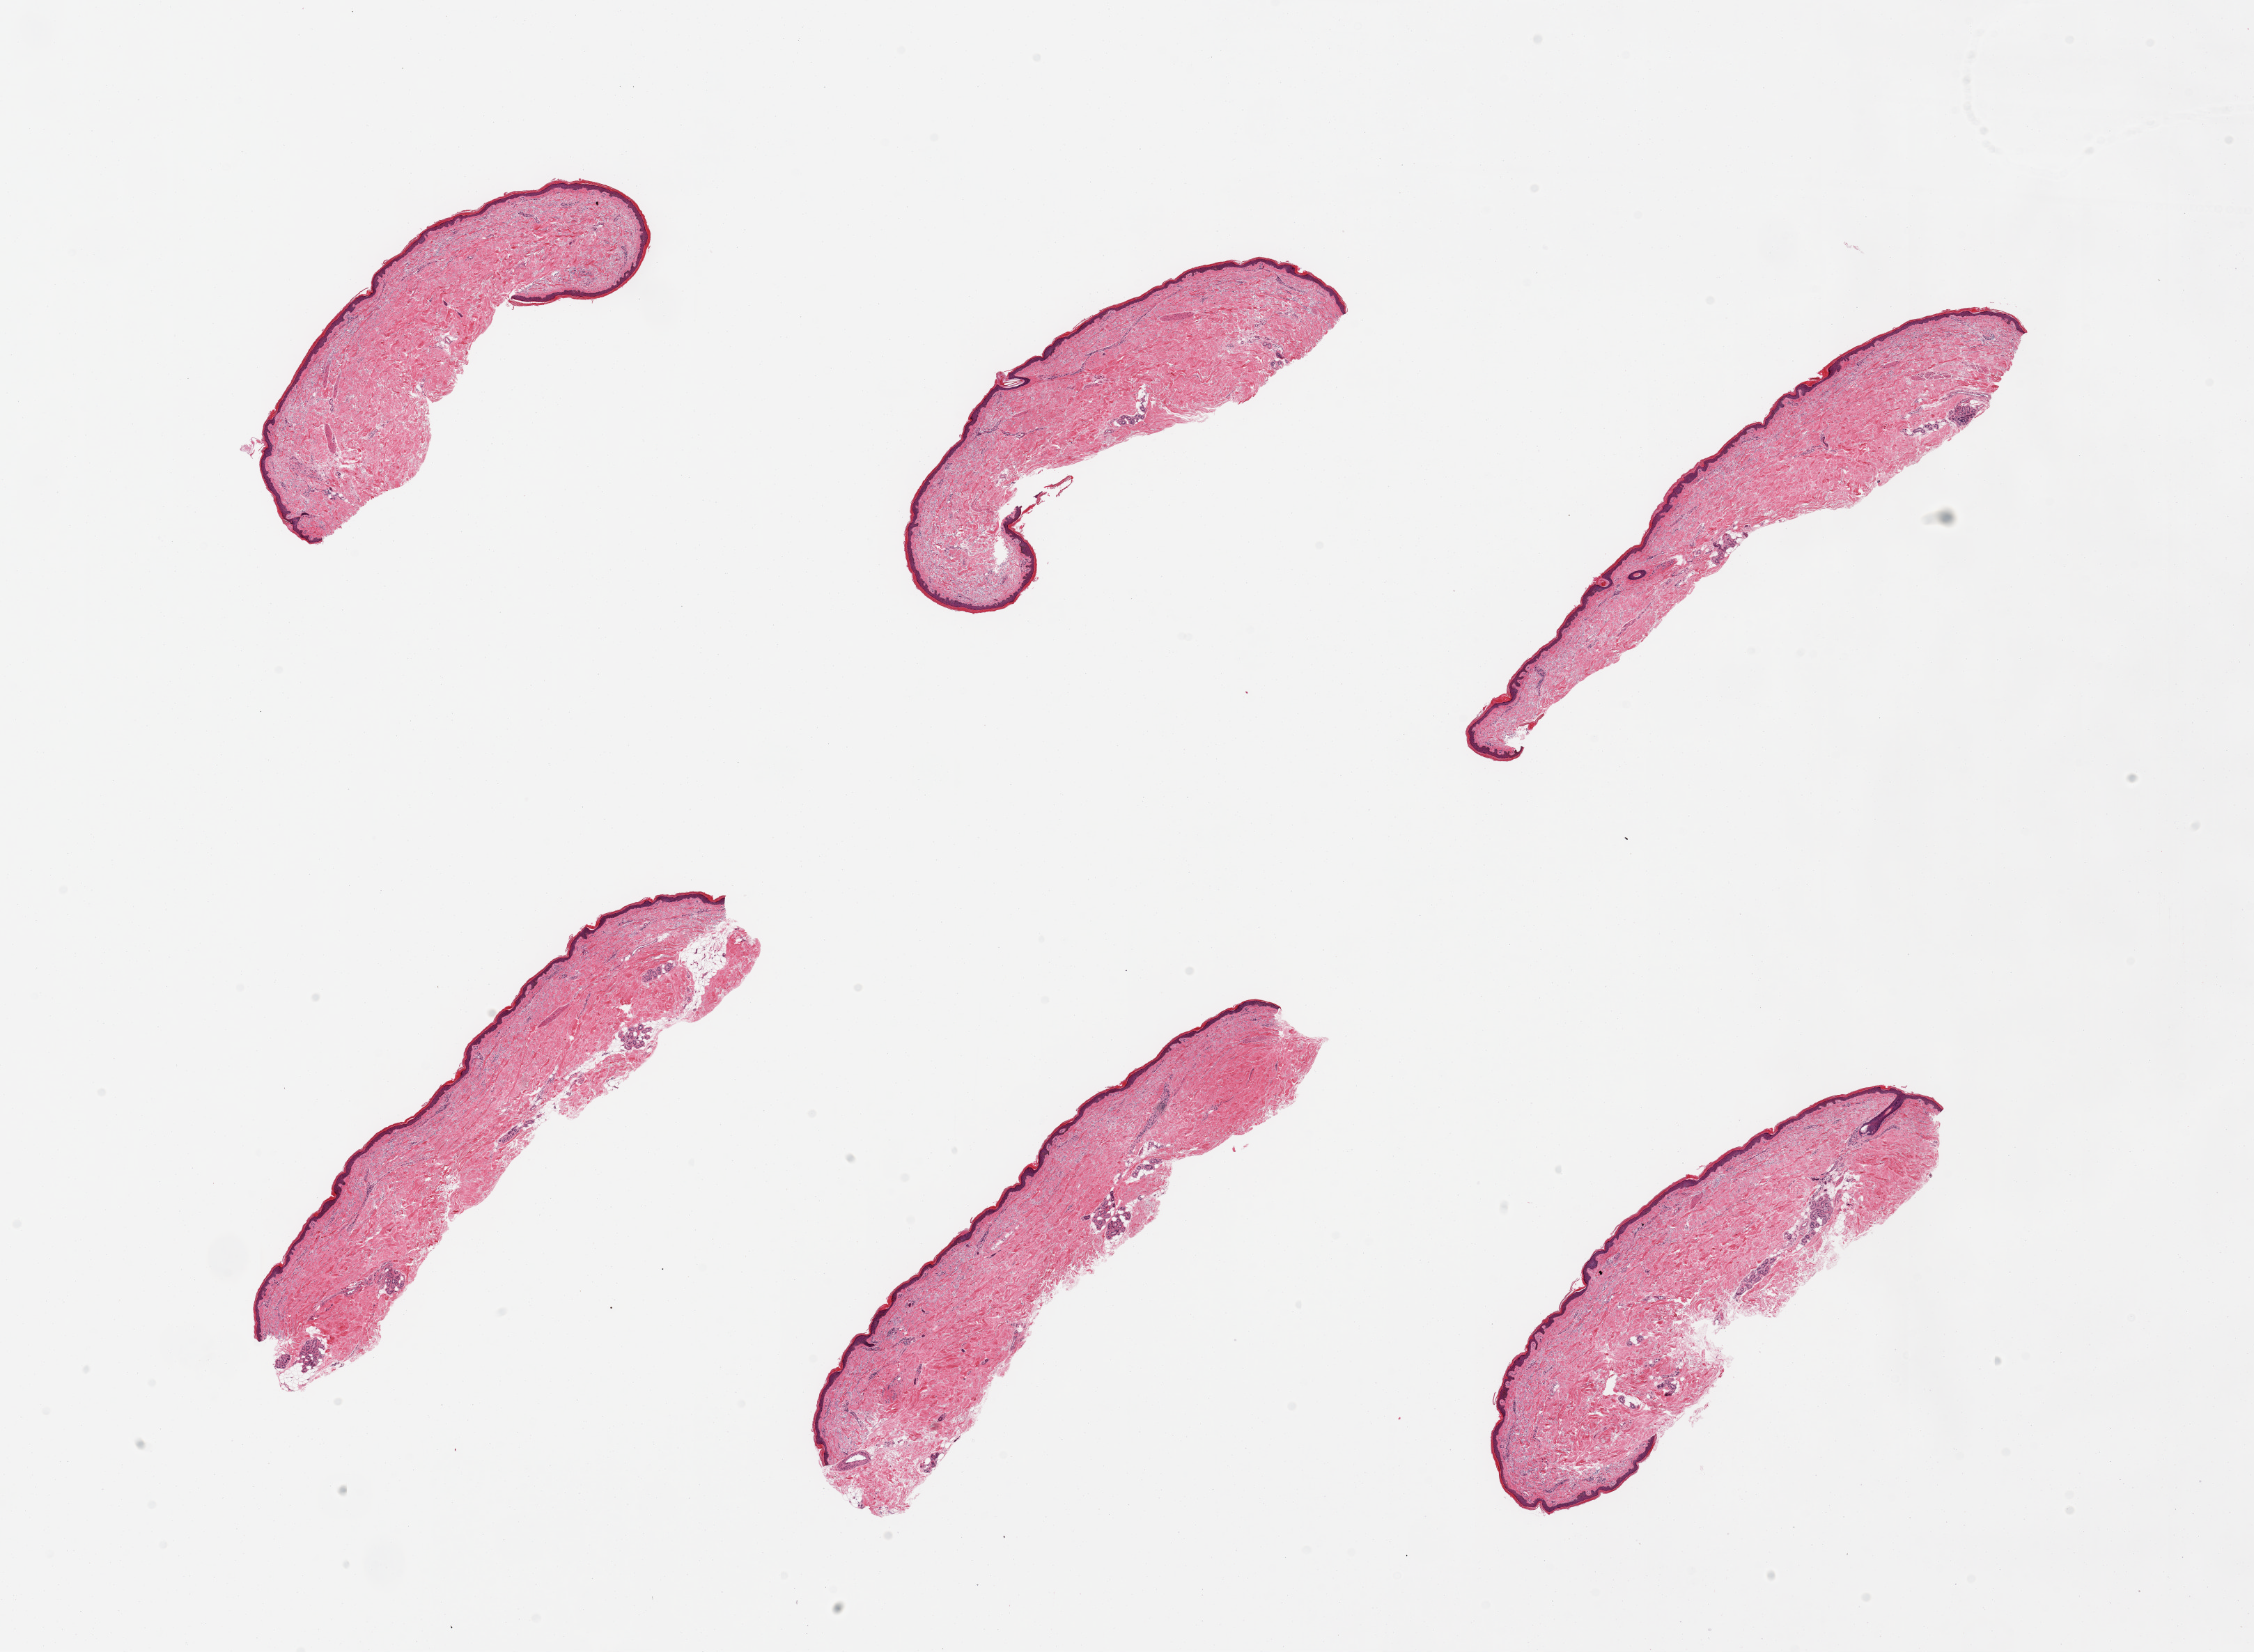
H&E whole-slide image, brightfield — shown as a low-resolution overview of the whole scanned area (about 25.6 x 18.8 mm, slide scanned at 20x), PAXgene-fixed paraffin-embedded (PFPE) section, sampled site (target tissue): skin of lower leg, donor tissue sample. Male donor.
Review note (as recorded): 6 pieces, minimal fat; squamous epithelium is ~40 microns.